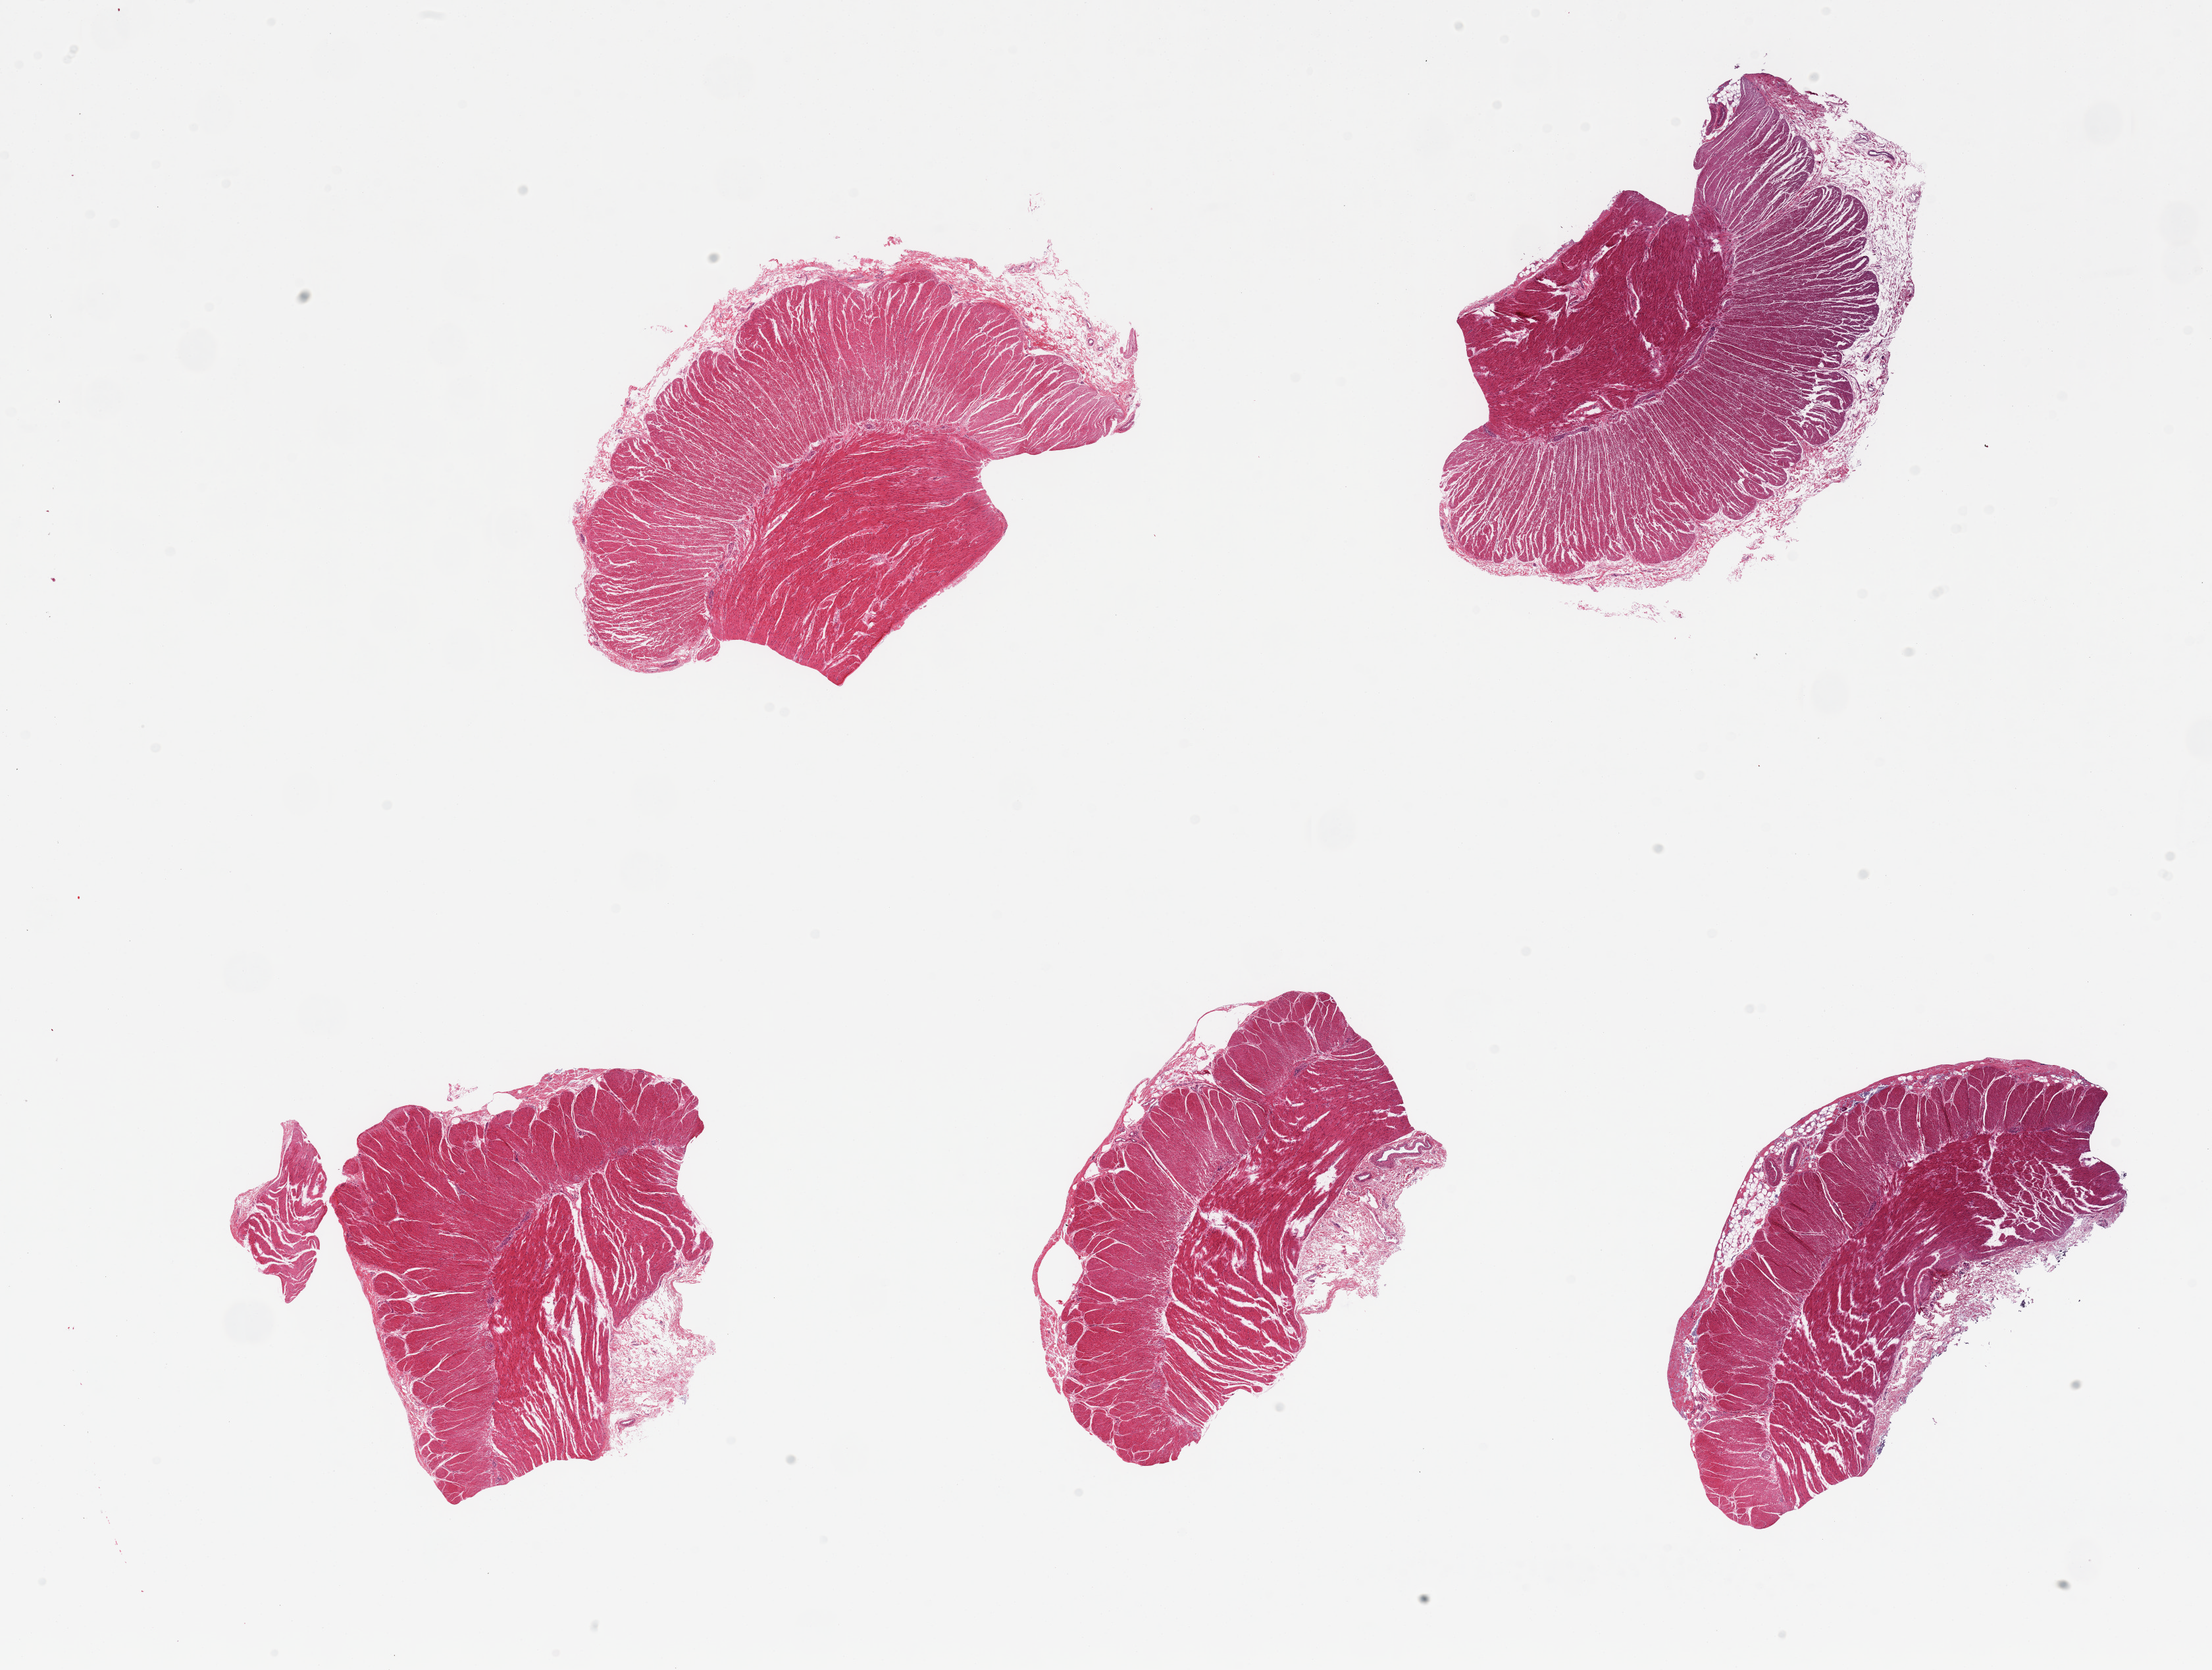
Digitized H&E-stained section, brightfield — whole scanned area (about 26.6 x 20.1 mm, slide scanned at 20x) shown as a low-resolution overview; PAXgene-fixed, paraffin-embedded tissue; sampled site (target tissue): sigmoid colon; donor tissue sample. Donor sex: female.
Reviewer comment on this tissue sample: 5 pieces; well dissected muscularis.